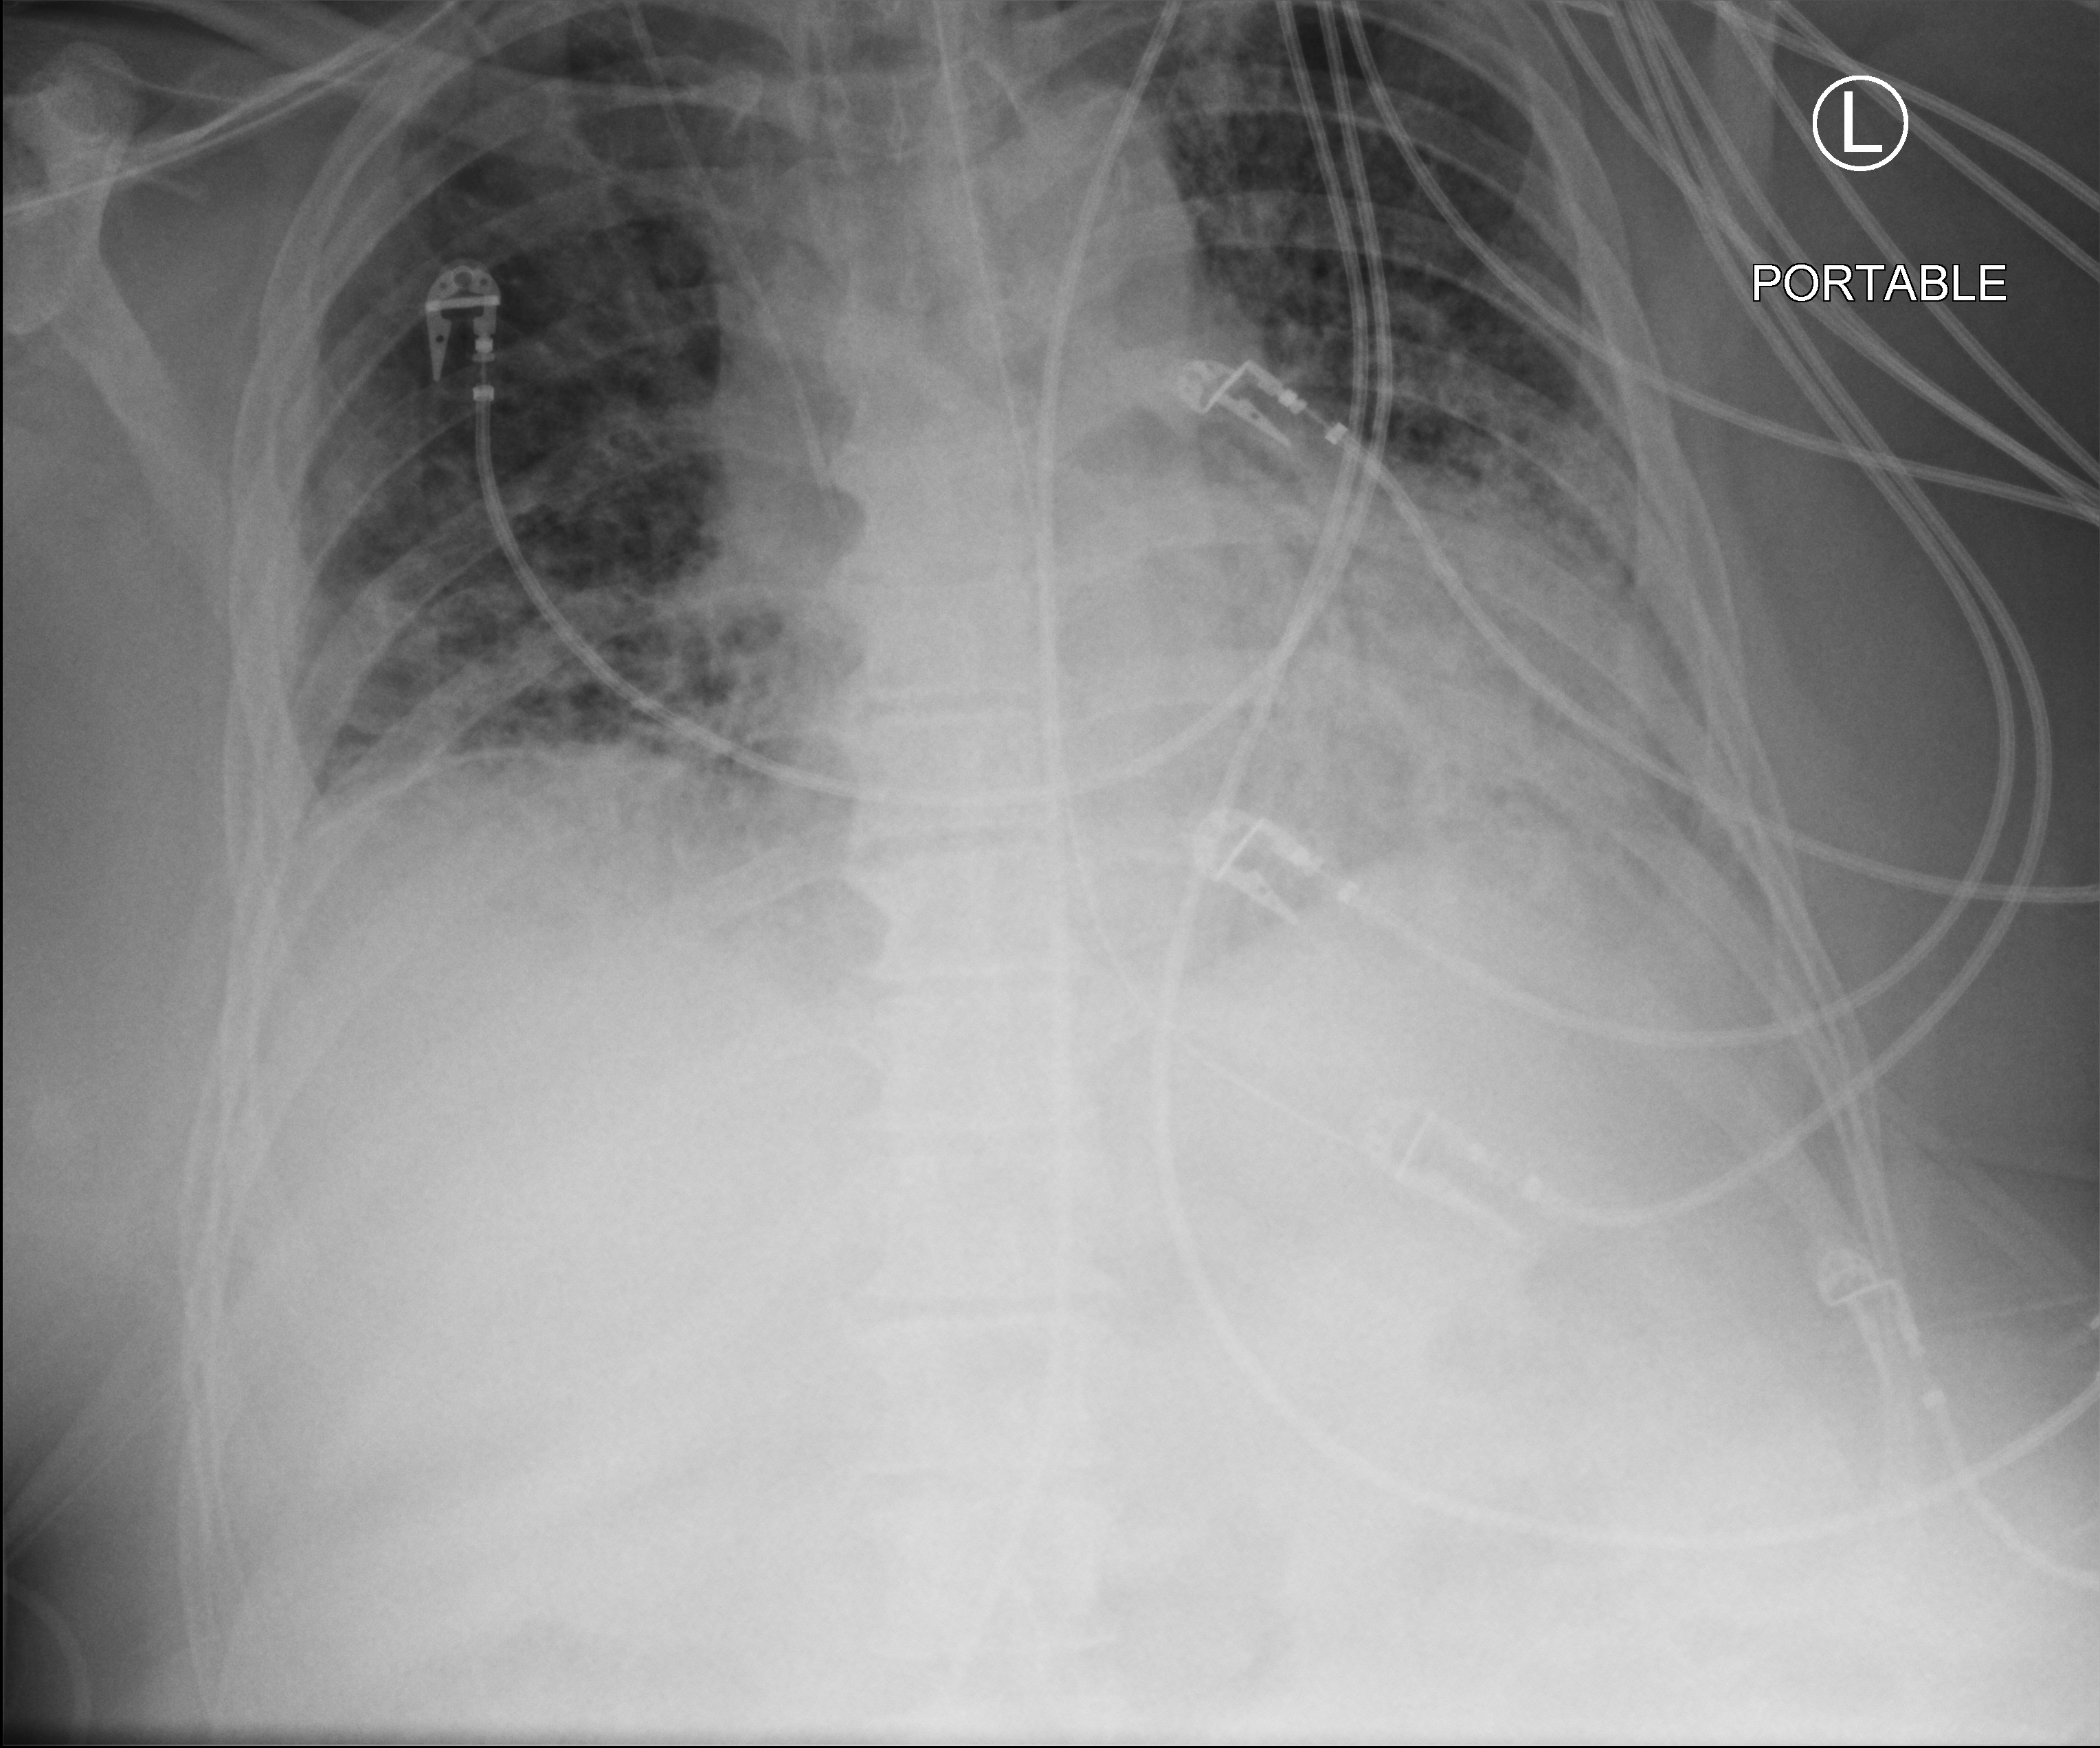
Bedside chest radiograph (computed radiography), anteroposterior (AP) projection. Male patient hospitalised with COVID-19, age 60–74 years.
Hospital-stay facts (about this admission, not read from this image; timing relative to this image not recorded): mechanically ventilated during this hospital stay: yes.